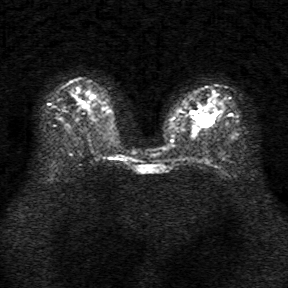
Breast MRI, one axial slice; position 16 of 34 along the scan axis; diffusion-weighted series; image 2 of 4 stored at this slice position (different b-values; order by instance number); 1.5 T; 5 mm slice thickness; 288 × 288 image matrix, field of view 340 × 340 mm. Female patient.
Structures marked on this image (manually delineated by an expert):
- tumour on diffusion-weighted imaging: bounding box (x1, y1, x2, y2) in pixels: (201, 114, 212, 125)